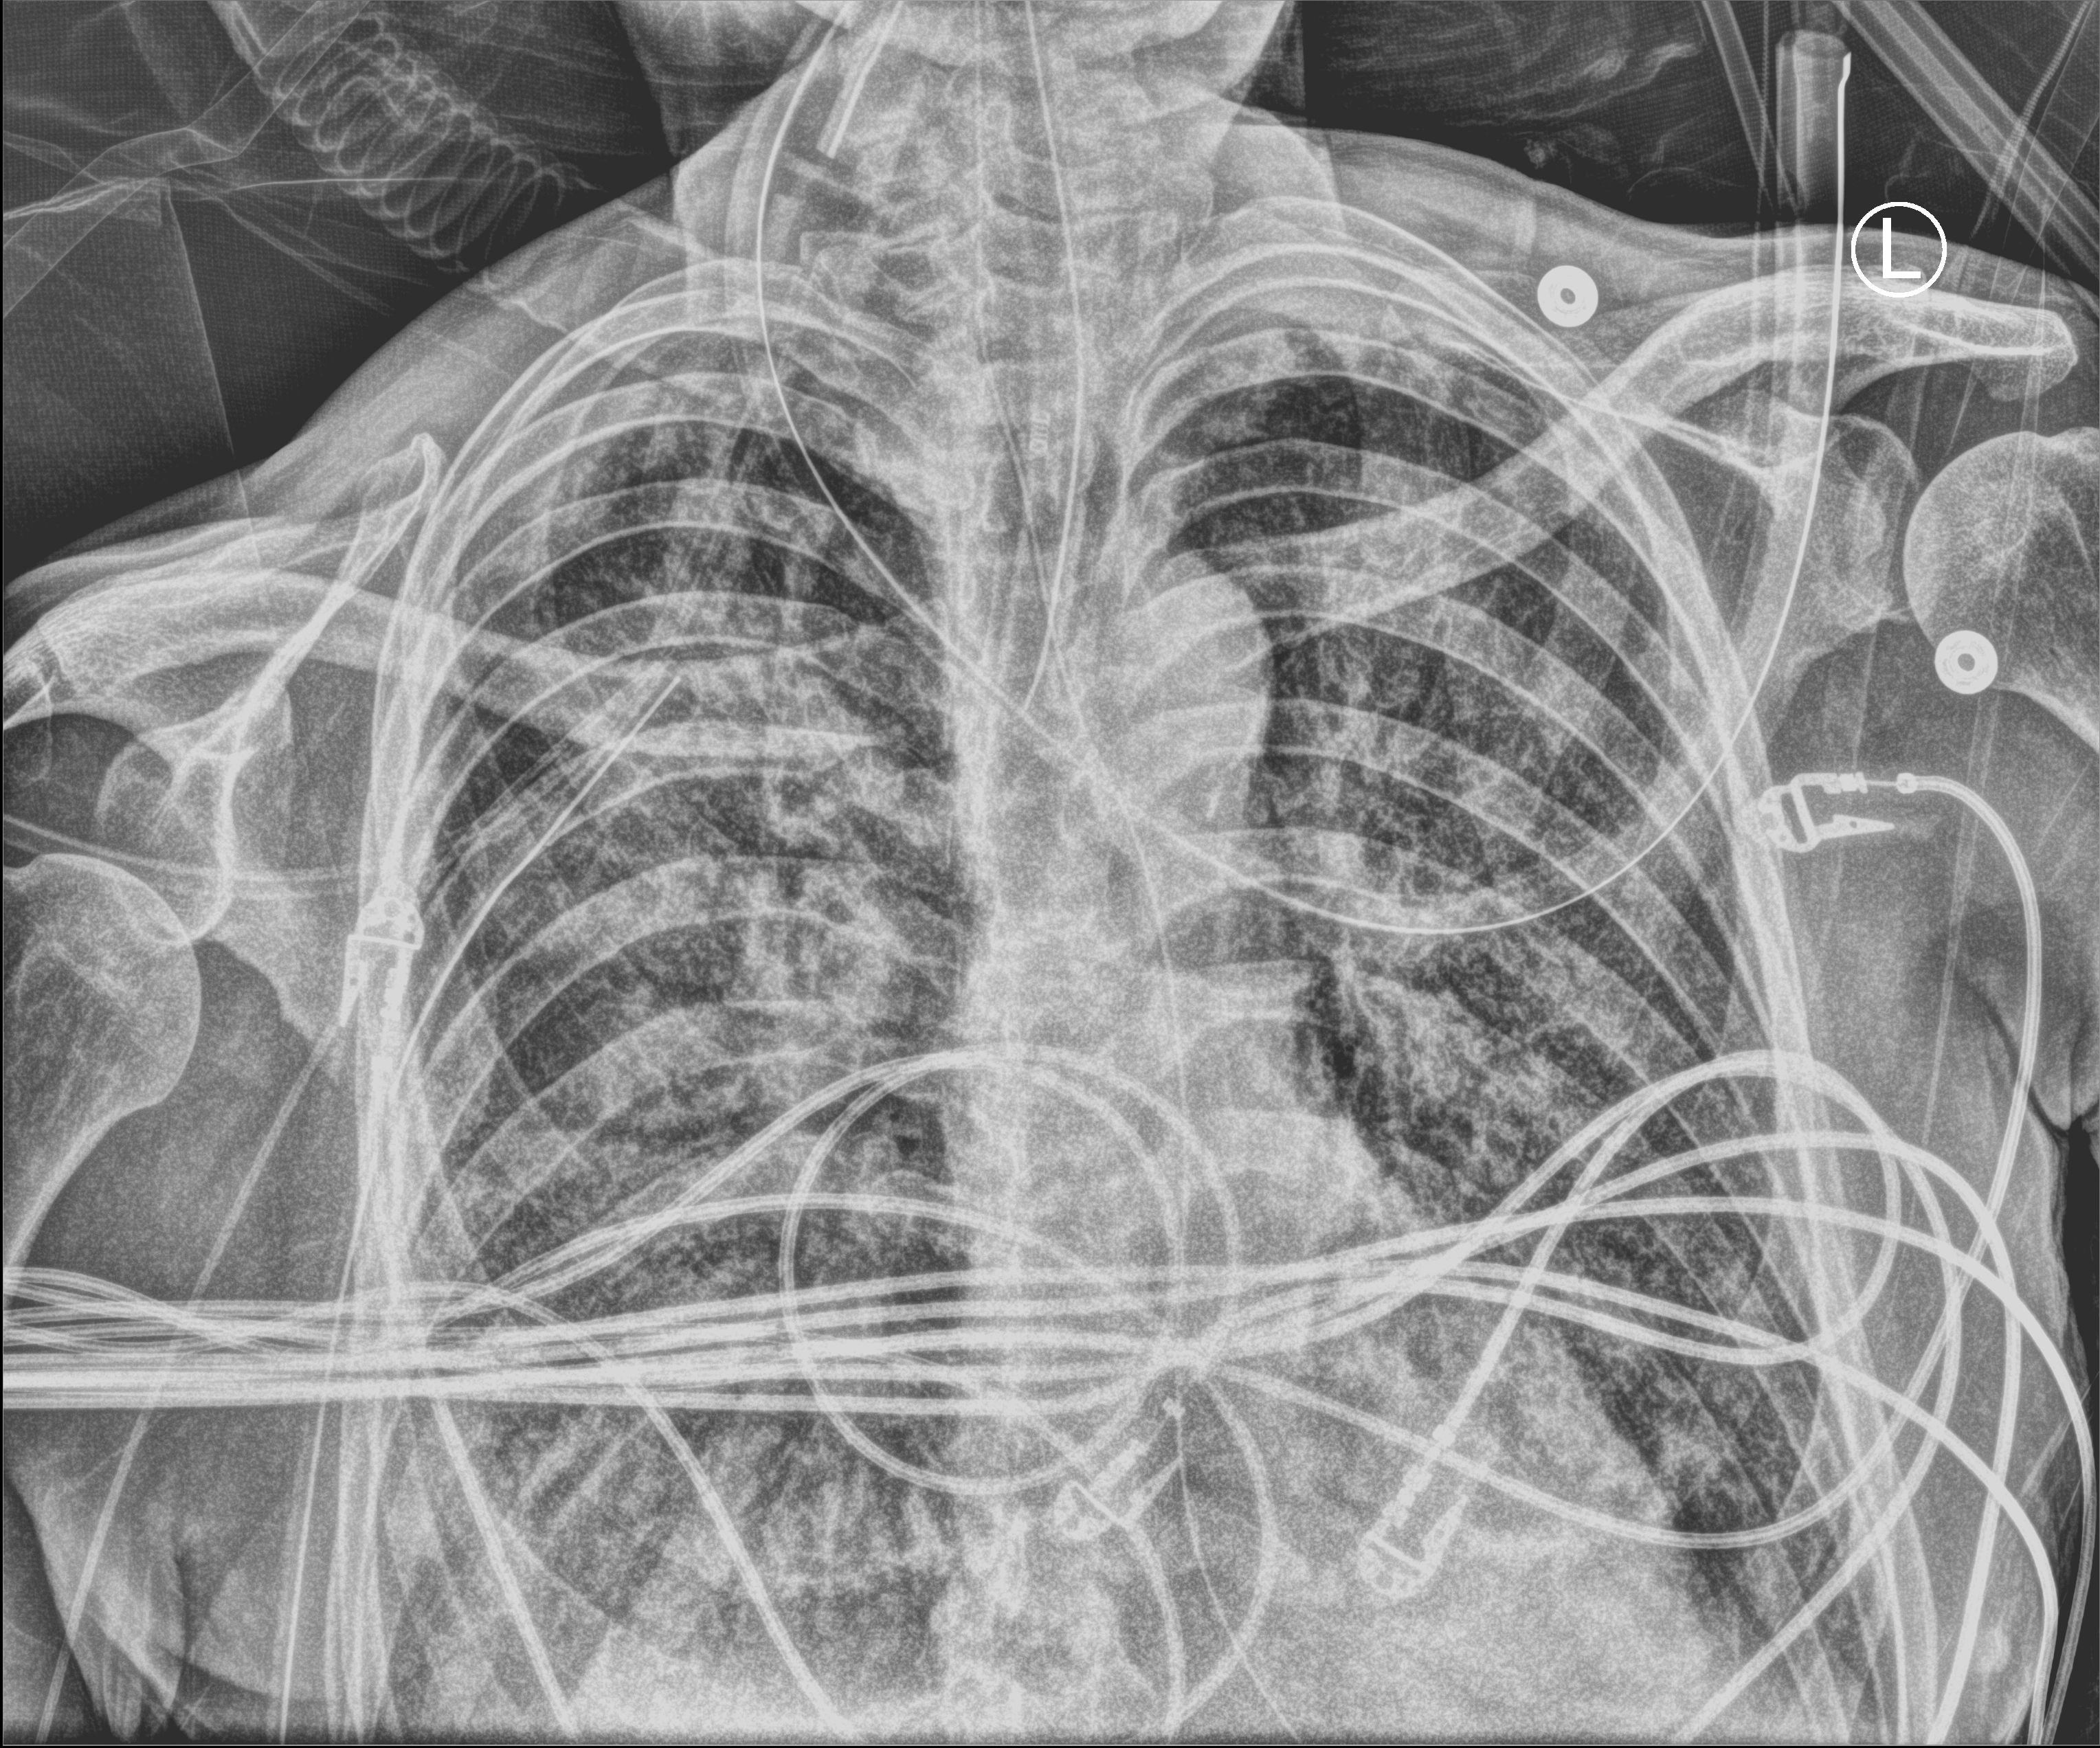
Portable chest radiograph. Patient hospitalised with COVID-19; male, aged 60–74 years.
Hospital-stay facts (about this admission, not read from this image; timing relative to this image not recorded): admitted to intensive care during this hospital stay: yes; mechanically ventilated during this hospital stay: yes; hypertension (admission record): no.